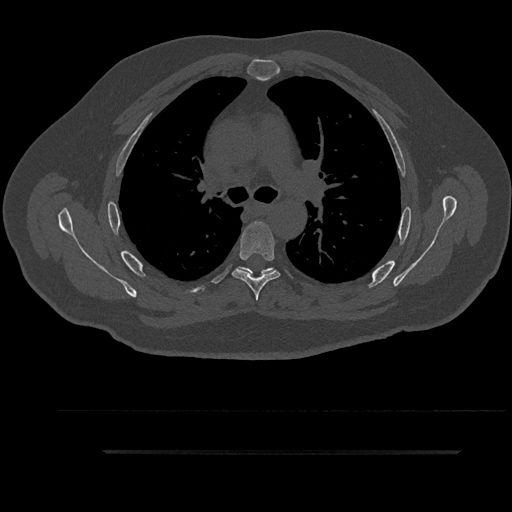
CT including the spine, one axial slice; reconstruction kernel Br40s/3; 120 kVp; bone window (W 1800 / L 400 HU); 512 × 512 image matrix, field of view 432 × 432 mm. Male patient, age 63 years. Case-level facts recorded for this patient, not image findings: primary cancer: renal; vertebrae with lytic lesions (as recorded): T8.
Outlined on this slice (semi-automatically segmented with operator editing):
- T5 vertebra: box from (x=232, y=221) to (x=281, y=301) px
- T6 vertebra: (x=242, y=268)–(x=276, y=278)